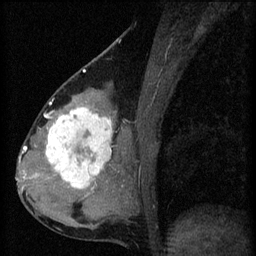
Breast MRI (dynamic contrast-enhanced), one sagittal slice. Position 28 of 60 along the scan axis. 3 images stored at this slice position (order not interpretable as contrast timing). 1.5 T. TE 4.2 ms, TR 8.2 ms. 256 × 256 image matrix. Female patient, age 37 years.
Annotated regions visible in this slice (semi-automatically segmented with operator editing):
- analysis volume of interest (the breast-tissue region the enhancement analysis was run in; not a lesion): bounding box (x1, y1, x2, y2) in pixels: (44, 100, 119, 197)
- tumour enhancement mask (voxels above the 70 % enhancement threshold inside the analysis volume of interest): (46, 108, 113, 189)